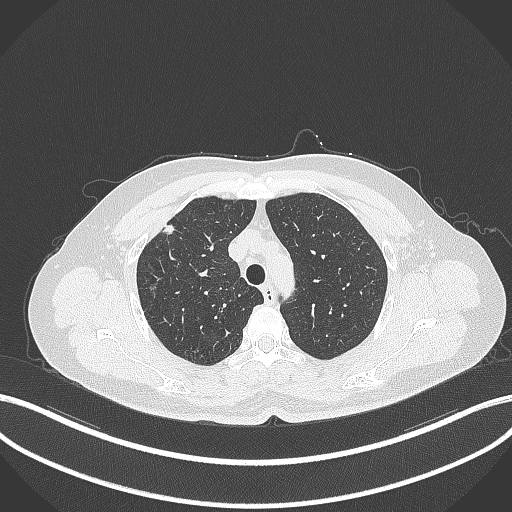
Chest CT, one axial slice. Reconstruction kernel B70f. Lung window (W 1500 / L -600 HU). 1 mm slice thickness. 512 × 512 image matrix, field of view 400 × 400 mm. Female patient, age 56 years. From the clinical record (not read from this slice): clinical TNM (as recorded): T1c N0 M0.
Outlined on this slice (rectangle marked by the reading radiologist):
- lung tumour (recorded histology: adenocarcinoma): bounding box <155,217,182,240> (left, top, right, bottom; pixels)